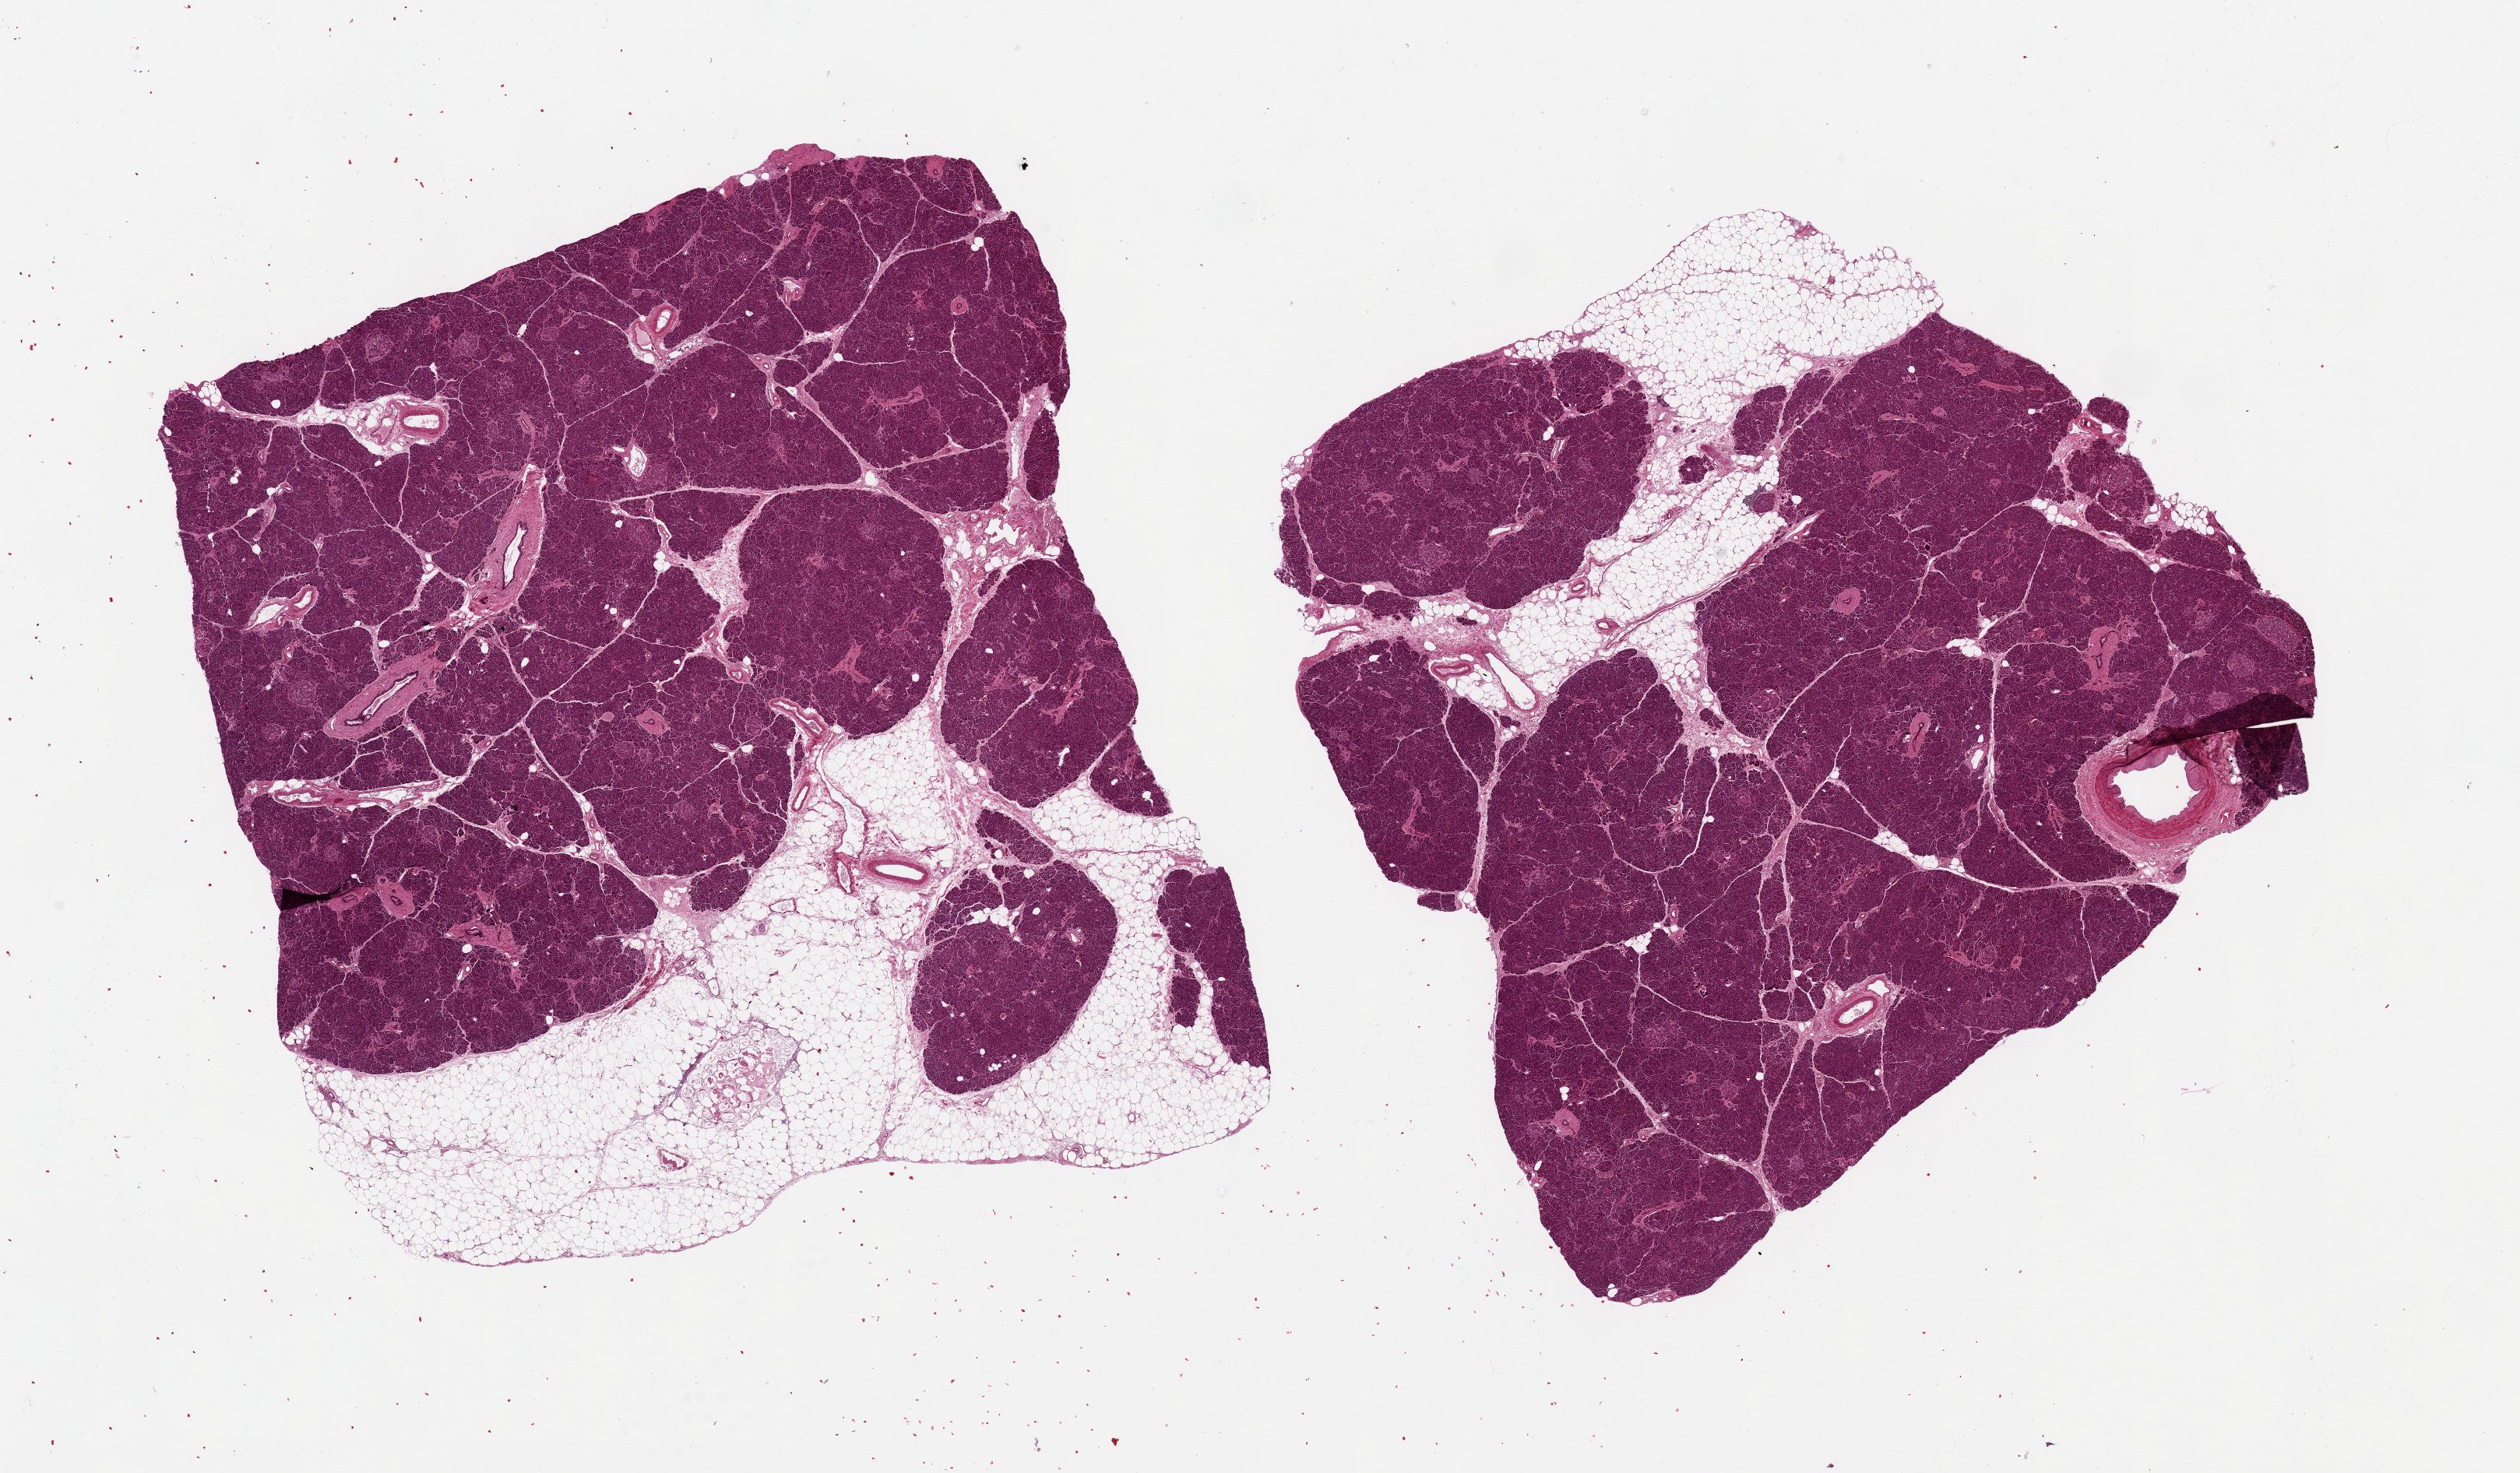
Whole-slide image, haematoxylin and eosin stain — whole scanned area (about 25.6 x 15.0 mm) shown as a low-resolution overview, PAXgene-fixed paraffin-embedded (PFPE) section, sampled site (target tissue): pancreas, donor tissue sample. Donor: male.
Reviewer comment on this tissue sample: 2 pieces, 11x10 & 10x8.5mm; 20-40% external adipose up to 2.6 mm thick.